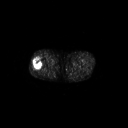
FDG PET of an extremity soft-tissue mass (from a PET/CT study), one axial slice; slice 237 of 267 in the series (ordered by position); 128 × 128 image matrix, field of view 700 × 700 mm. Male patient, age 43 years. Case-level facts recorded for this patient, not image findings: histological type: poorly differentiated synovial sarcoma; grade: high; site of the primary tumour: right buttock.
Structures marked on this image (expert contour drawn on MRI and transferred to this co-registered scan by the dataset authors):
- gross tumour volume including surrounding oedema: bounding box <32,57,43,70> (left, top, right, bottom; pixels)
- gross tumour volume (mass): <33,58,43,70>